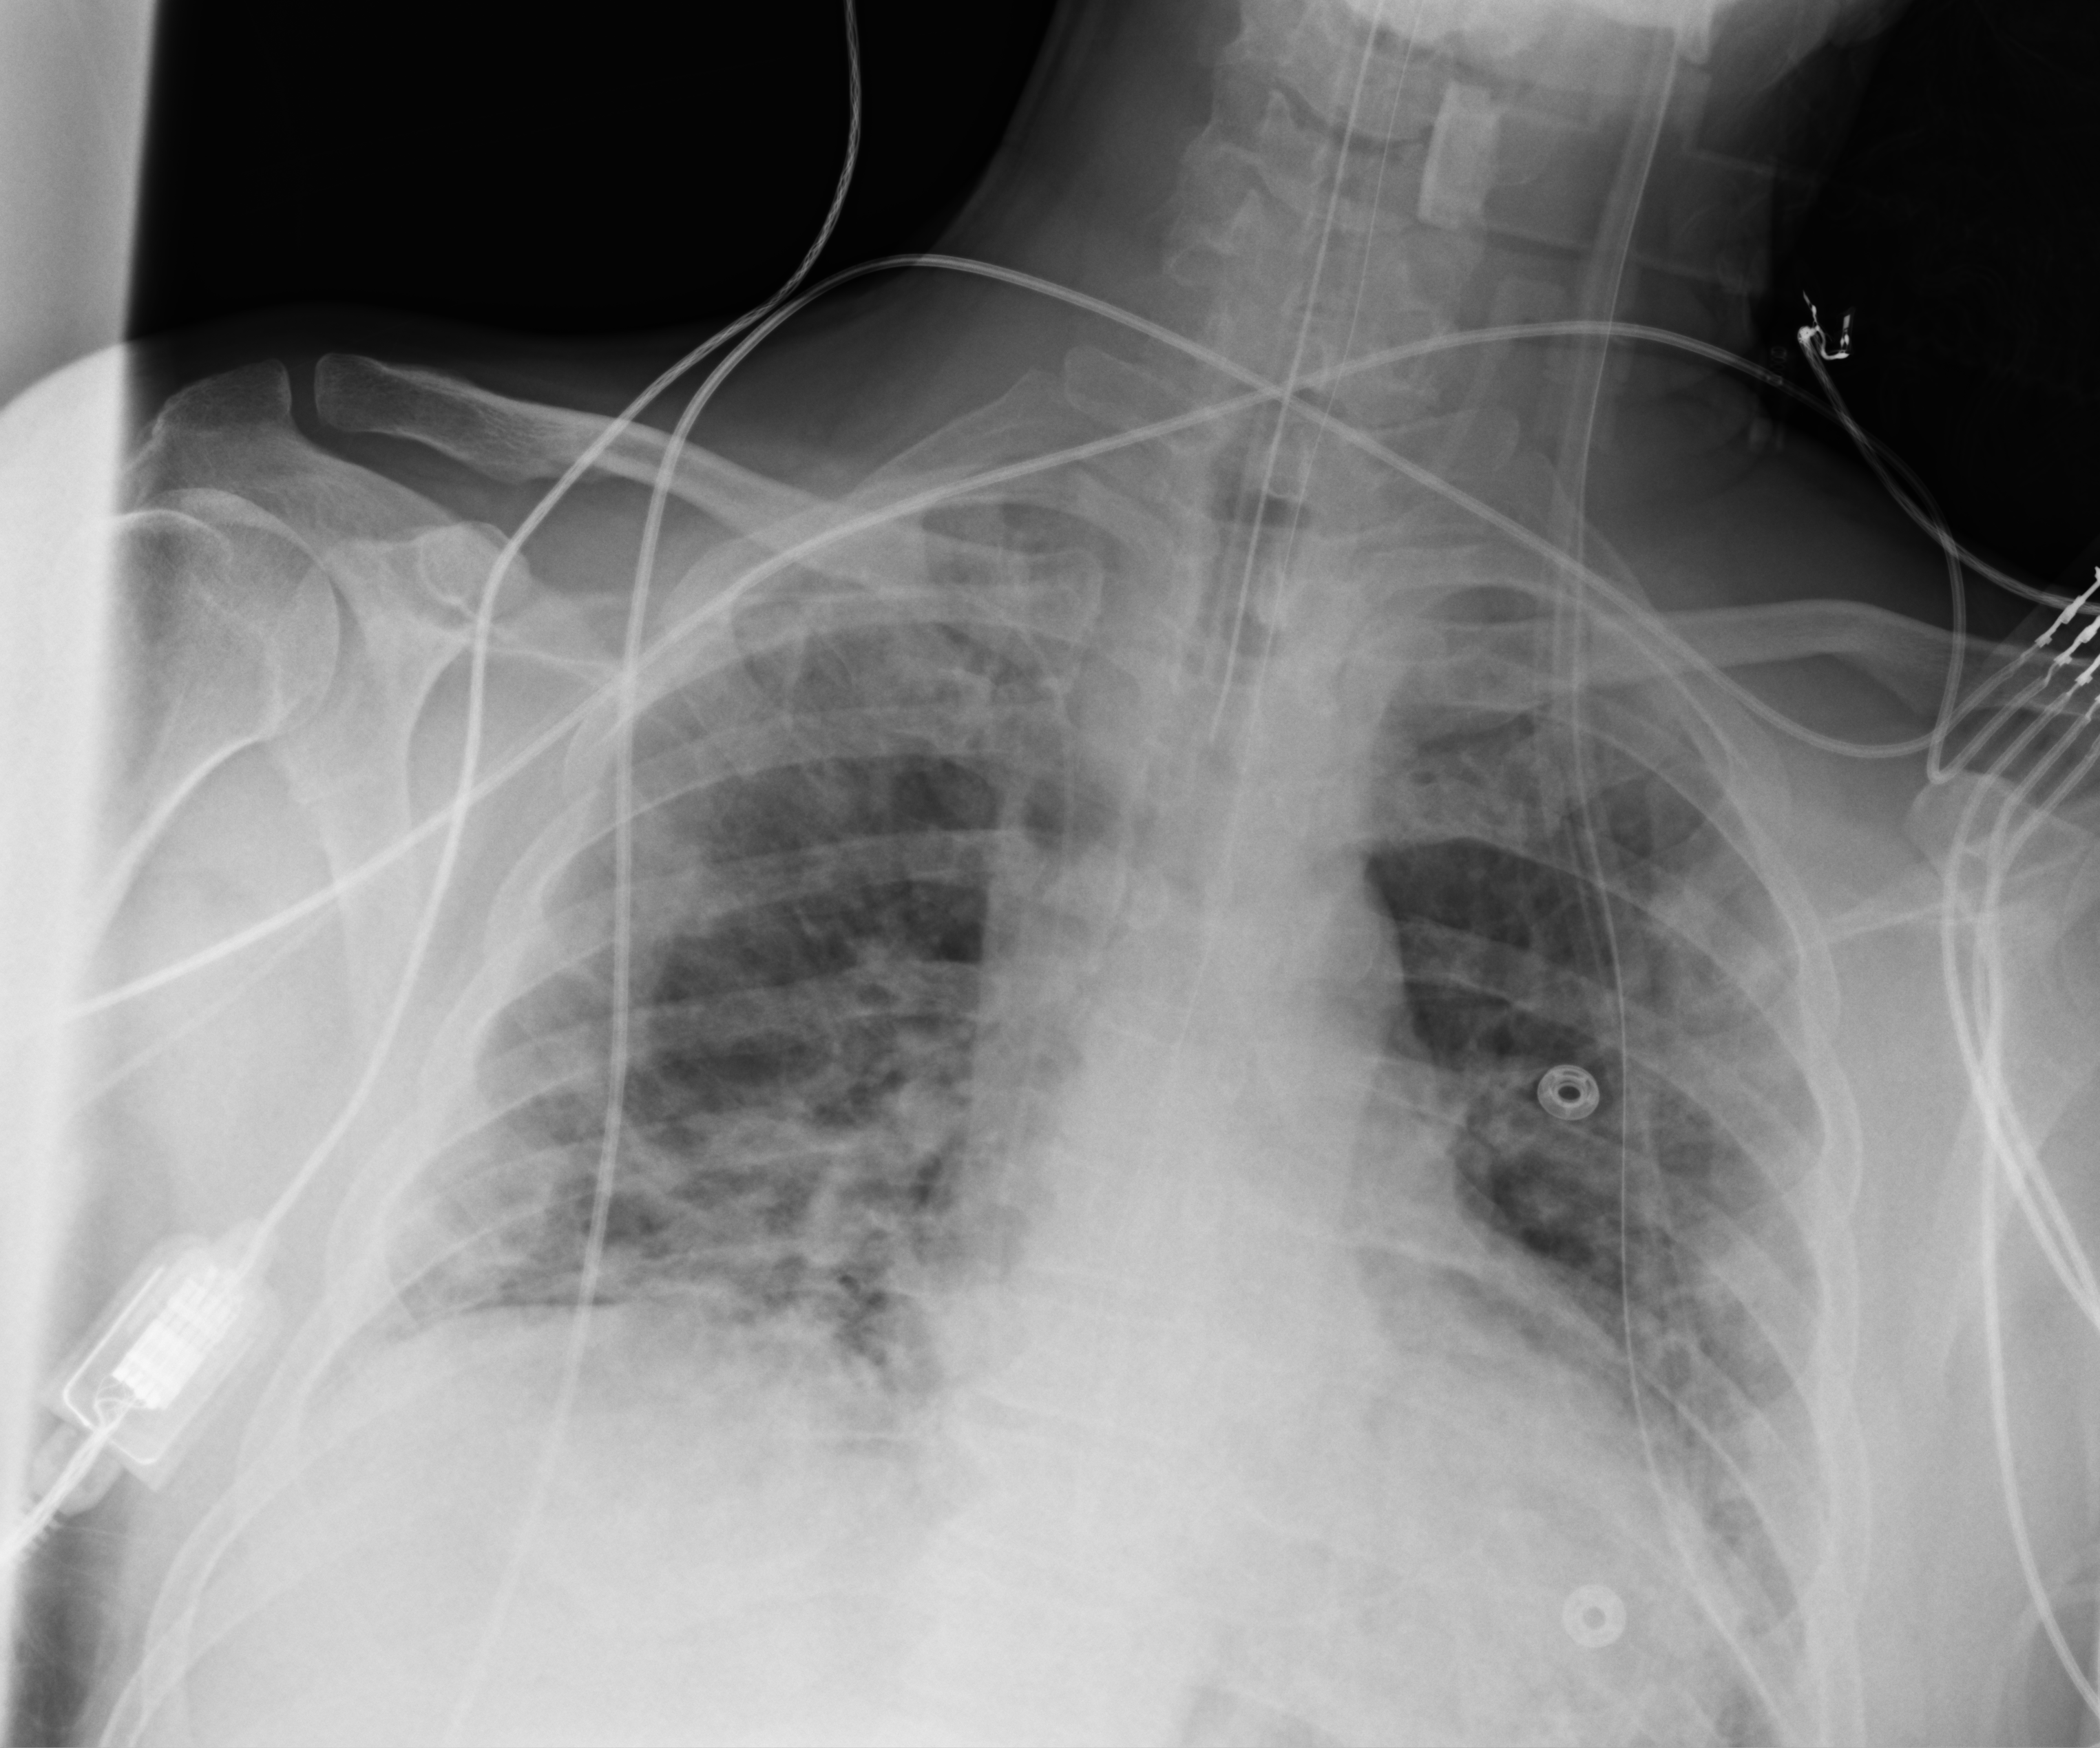
Bedside chest radiograph (computed radiography); anteroposterior (AP) projection. Male patient hospitalised with COVID-19, age 18–59 years.
Admission-level facts for this patient (not findings on this image; timing relative to this image not recorded):
- length of hospital stay: 32 days